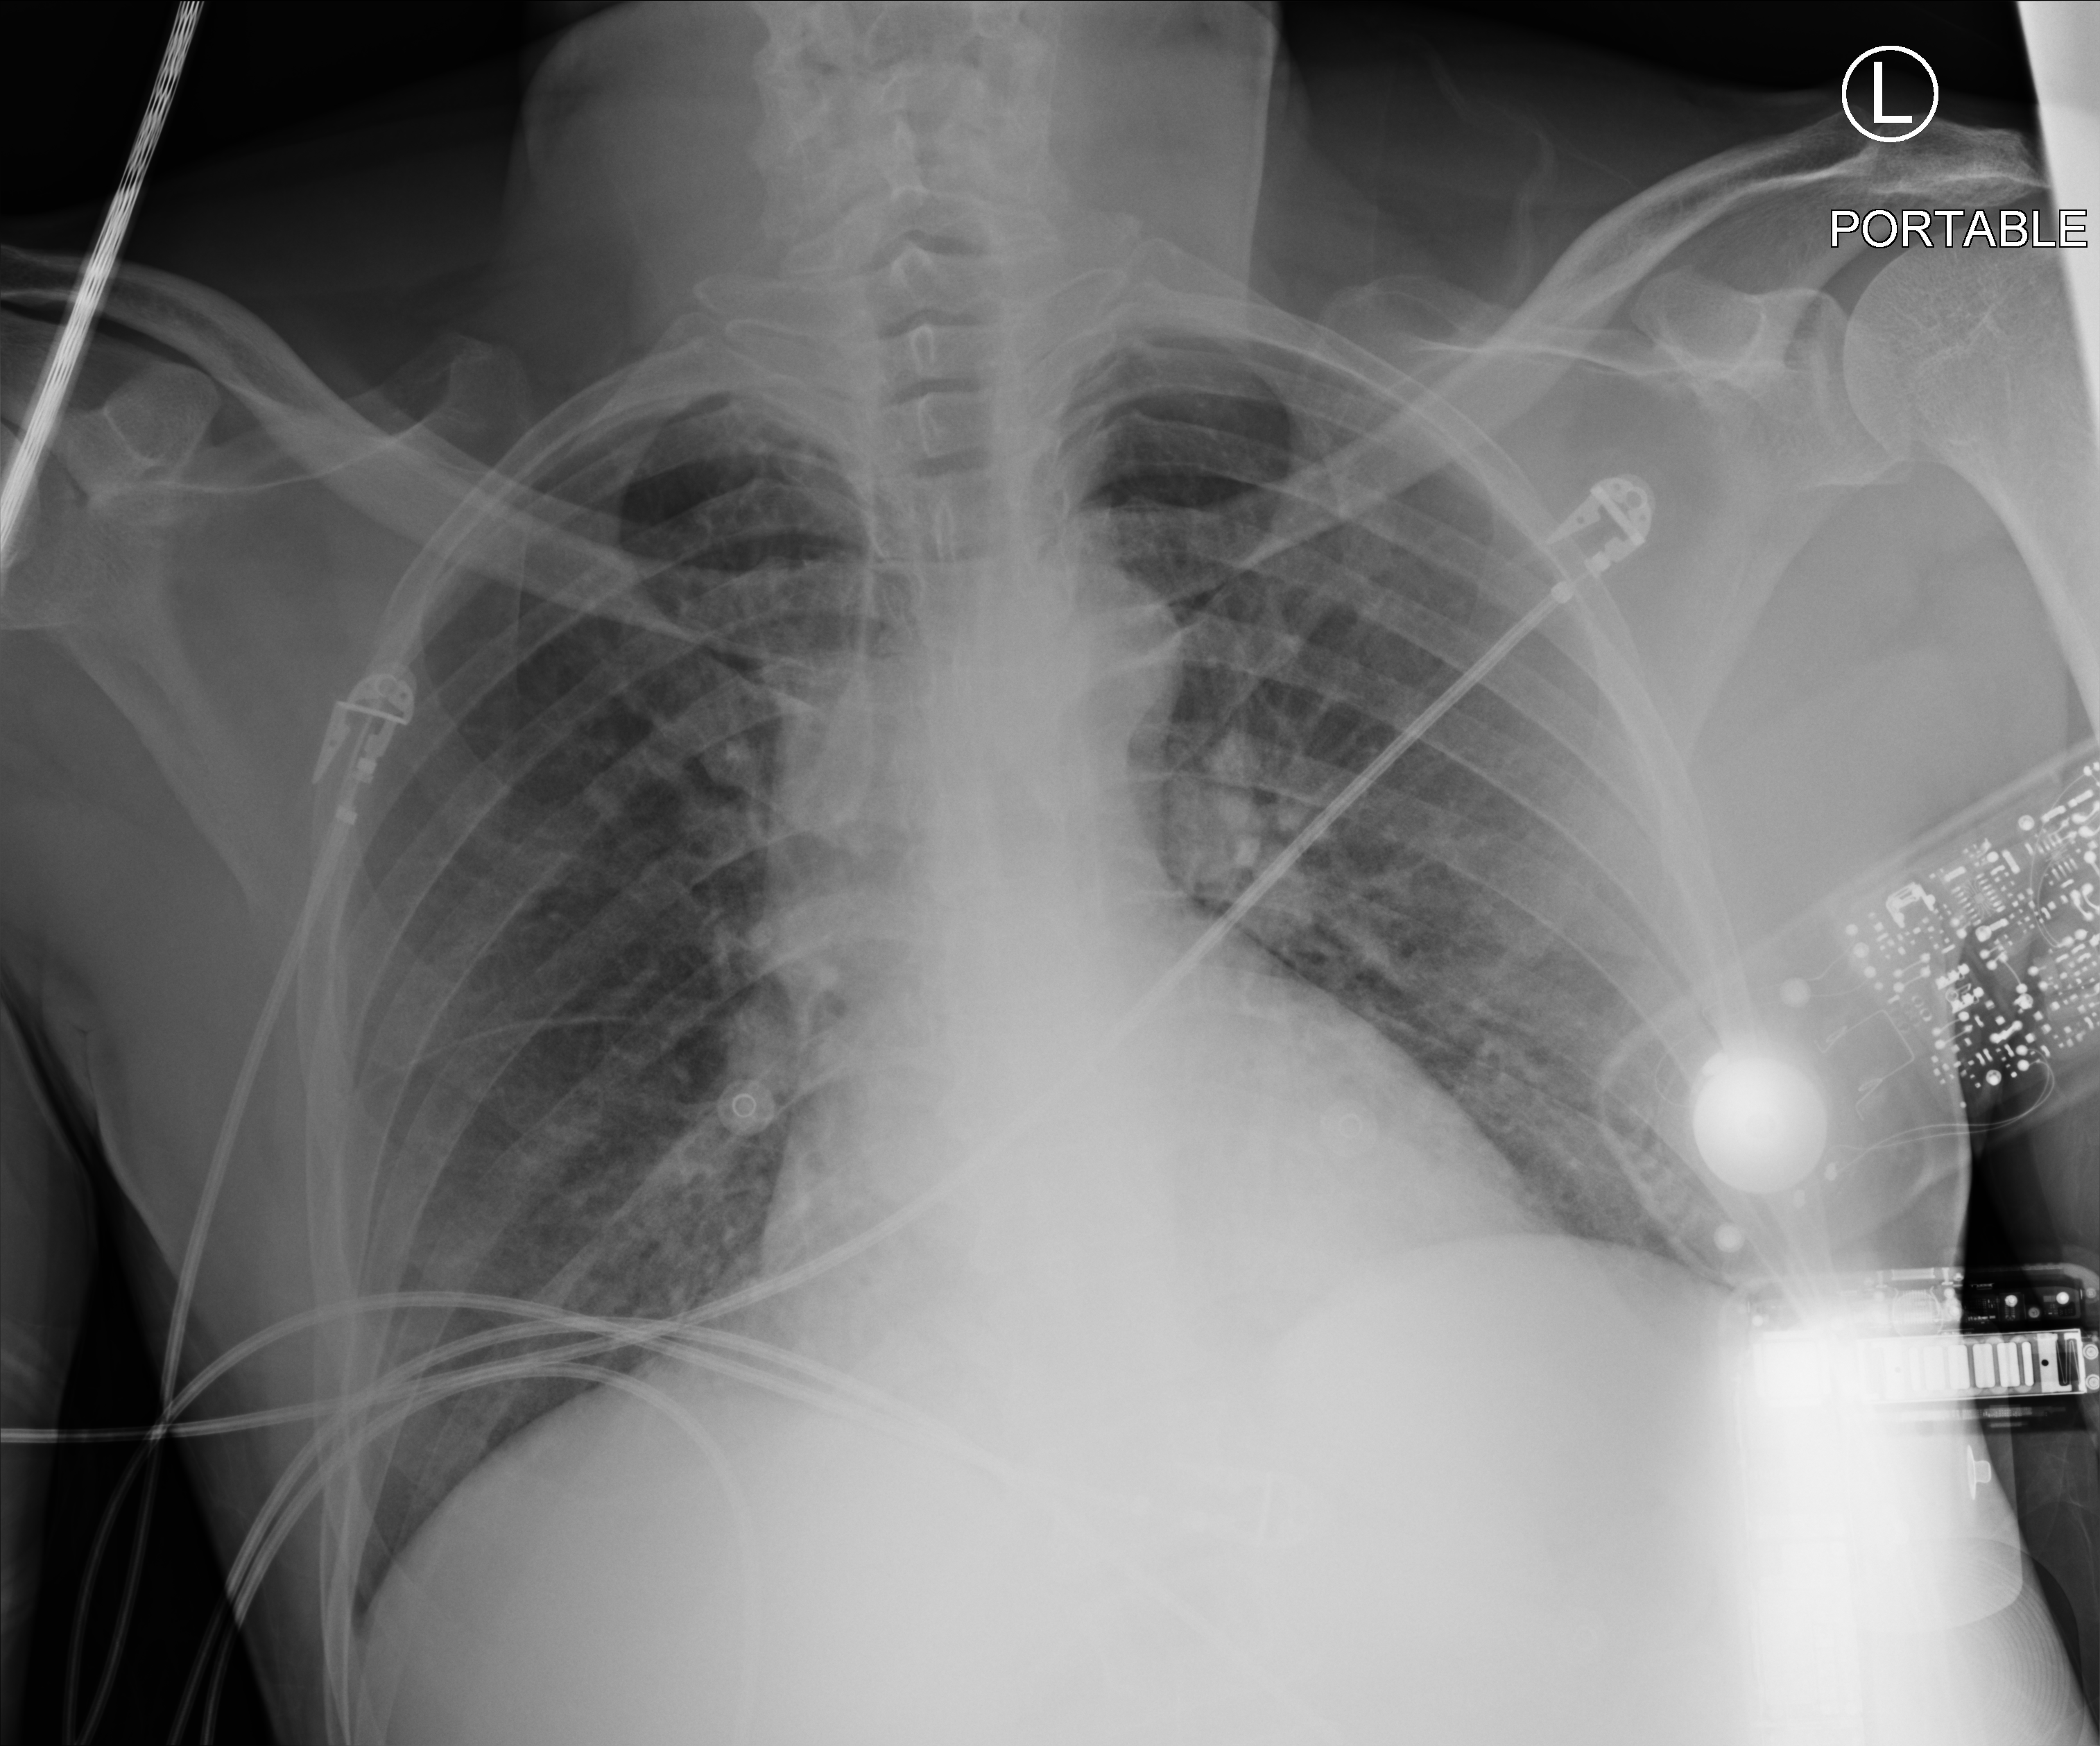
Portable chest radiograph. Male patient hospitalised with COVID-19, age 18–59 years.
Admission-level facts for this patient (not findings on this image; timing relative to this image not recorded): mechanically ventilated during this hospital stay: yes; hypertension (admission record): no; admitted to intensive care during this hospital stay: yes.